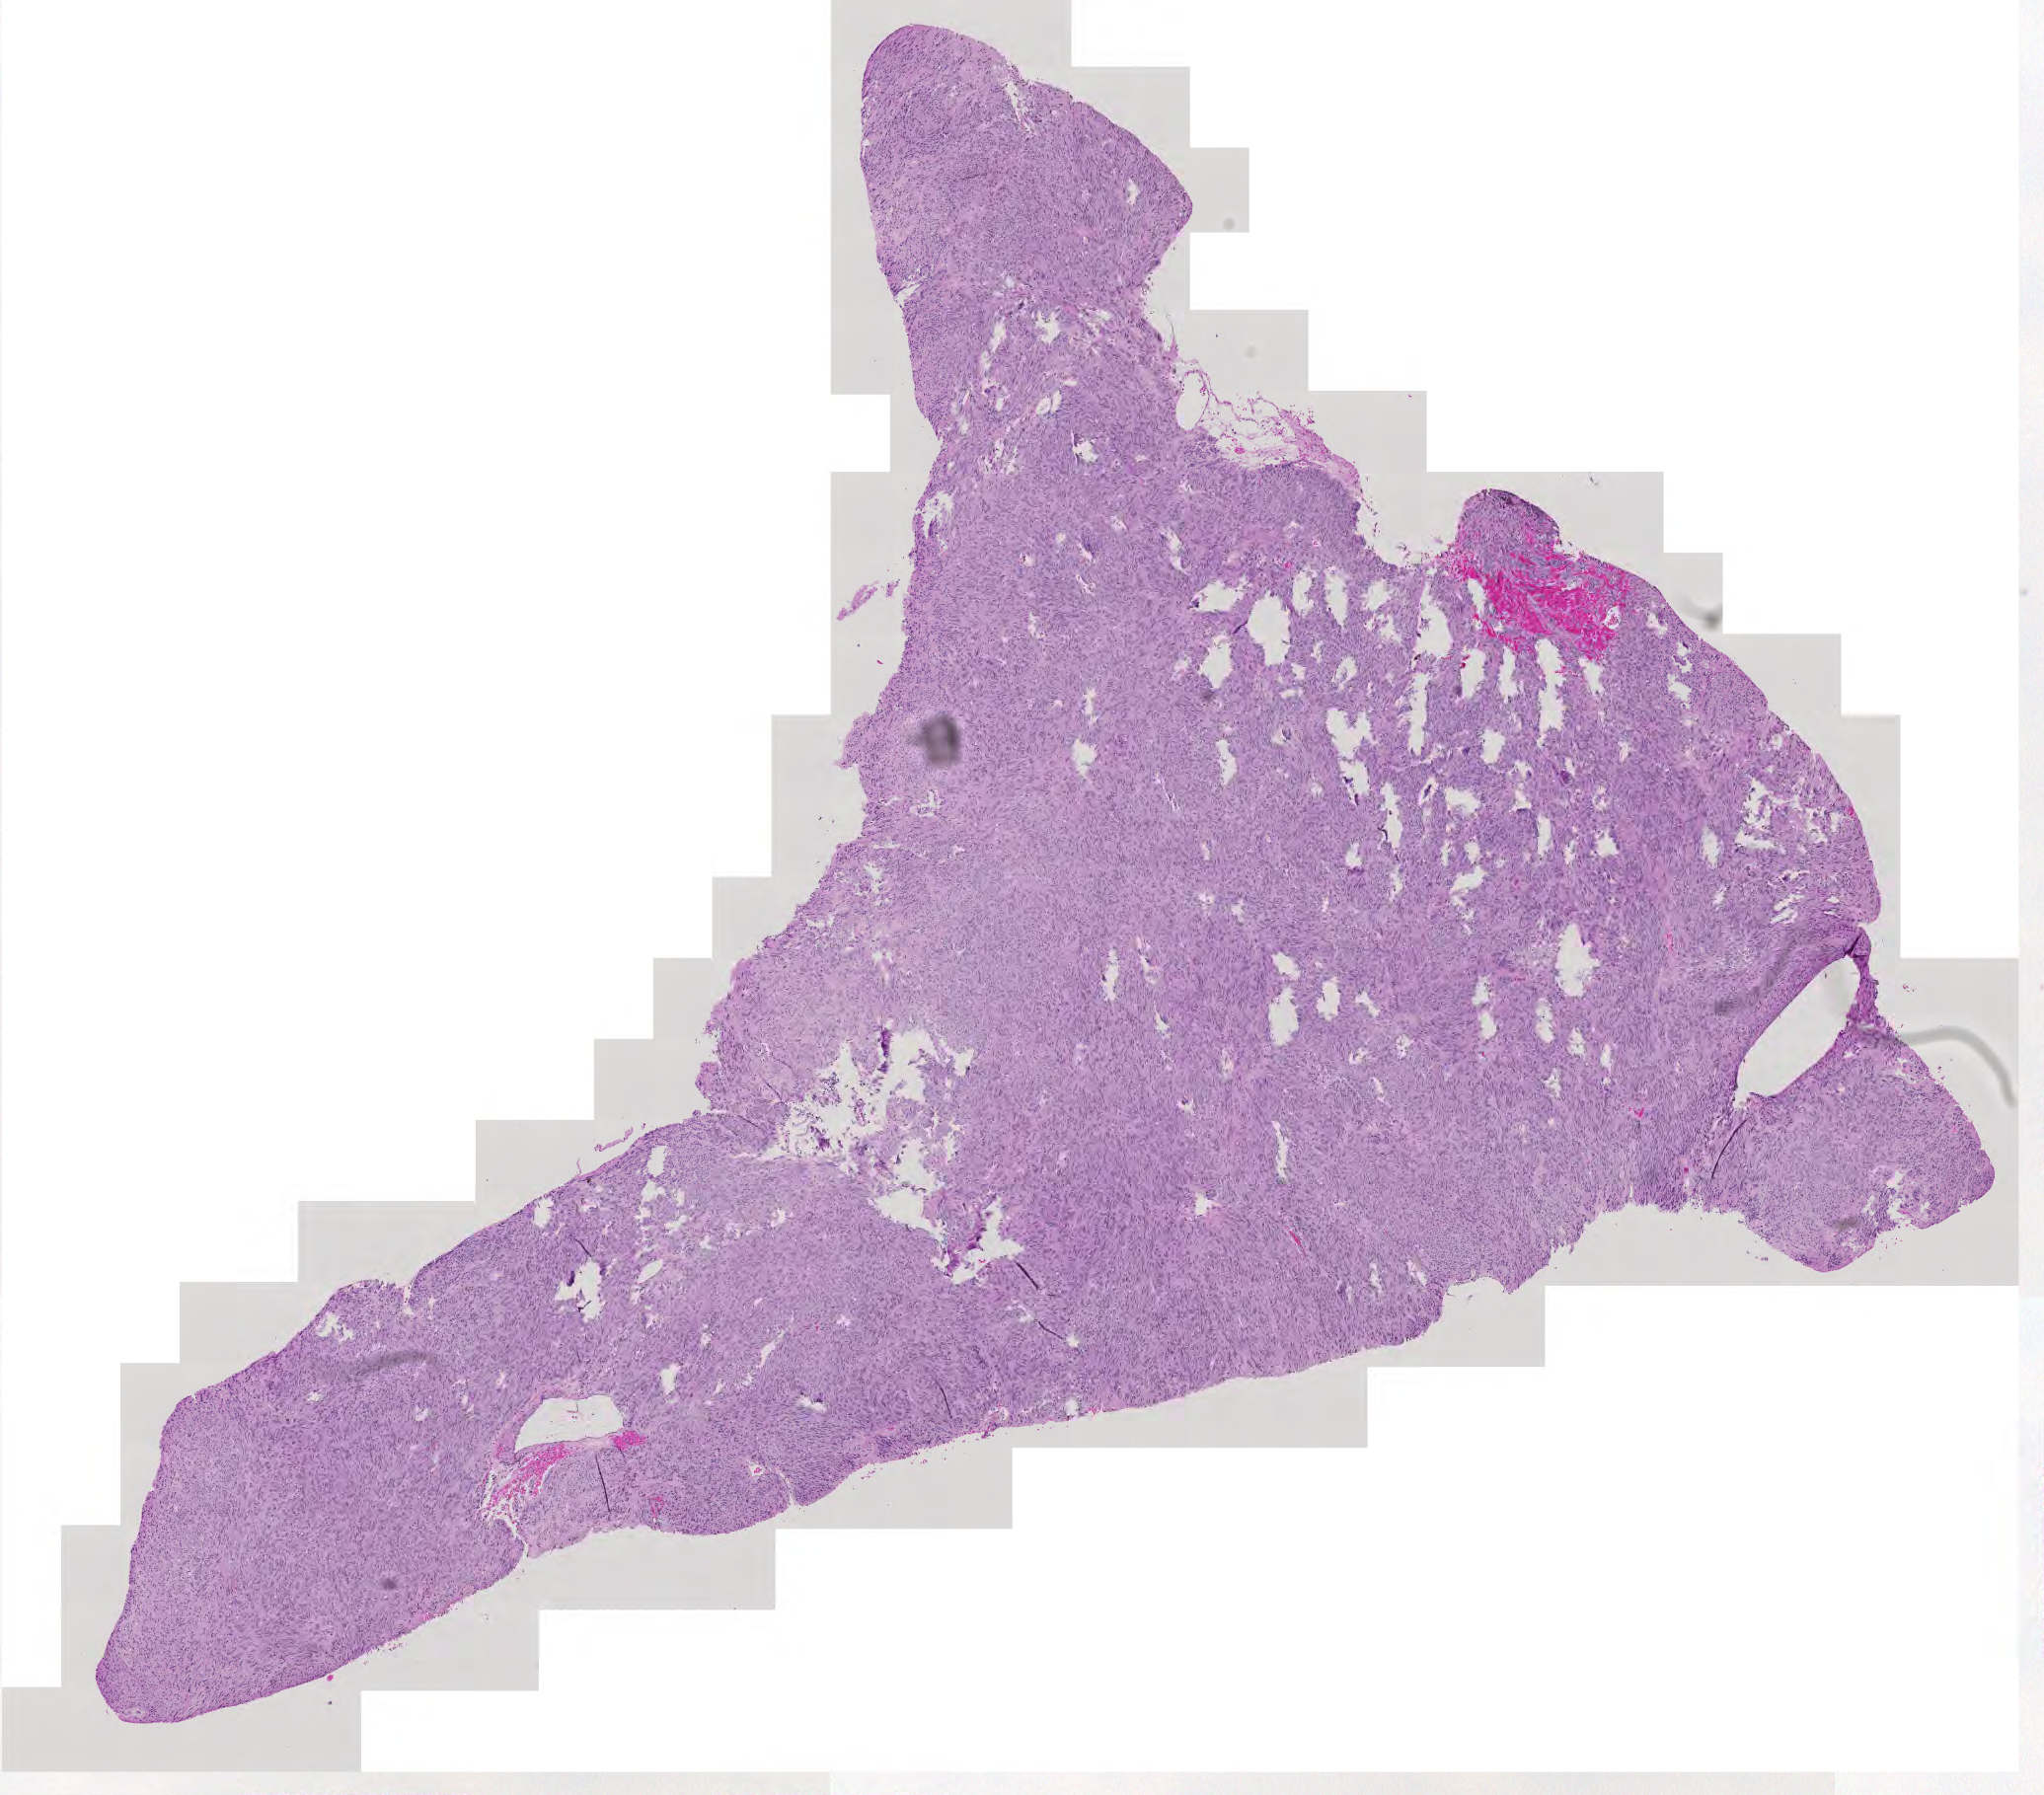
Whole-slide histology image, Hematoxylin and eosin (H&E) stained — shown as a low-resolution overview of the whole scanned area (about 10.7 x 9.4 mm). Patient: male, age 87 years.
Patient diagnosis (cohort enrolment): sarcoma (site not recorded at cohort level).